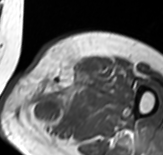
MRI of an extremity soft-tissue mass, one axial slice. MR volume resampled by the dataset authors to the PET/CT grid (not the native acquisition matrix). 3.27 mm slice thickness. 163 × 155 image matrix, field of view 159 × 151 mm. Female patient. From the clinical record (not read from this slice): histological type: pleomorphic leiomyosarcoma; grade: high; site of the primary tumour: left thigh.
Structures marked on this image (expert contour drawn on MRI and transferred to this co-registered scan by the dataset authors):
- gross tumour volume including surrounding oedema: bounding box (x1, y1, x2, y2) in pixels: (26, 63, 100, 134)